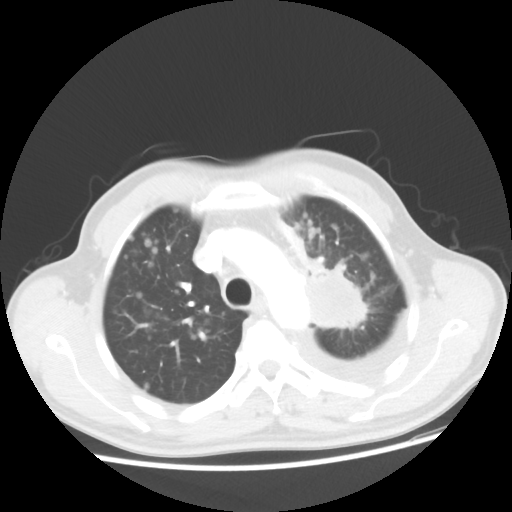
Chest CT, one axial slice; position 36 of 48 along the scan axis; 100 kVp; lung window (W 1500 / L -600 HU); 5 mm slice thickness; 512 × 512 image matrix, field of view 362 × 362 mm. Male patient, age 55 years. Case-level facts recorded for this patient, not image findings: clinical TNM (as recorded): T2 N3 M1a.
Annotated regions visible in this slice (rectangle marked by the reading radiologist):
- lung tumour (recorded histology: squamous cell carcinoma): bounding box <299,259,367,341> (left, top, right, bottom; pixels)